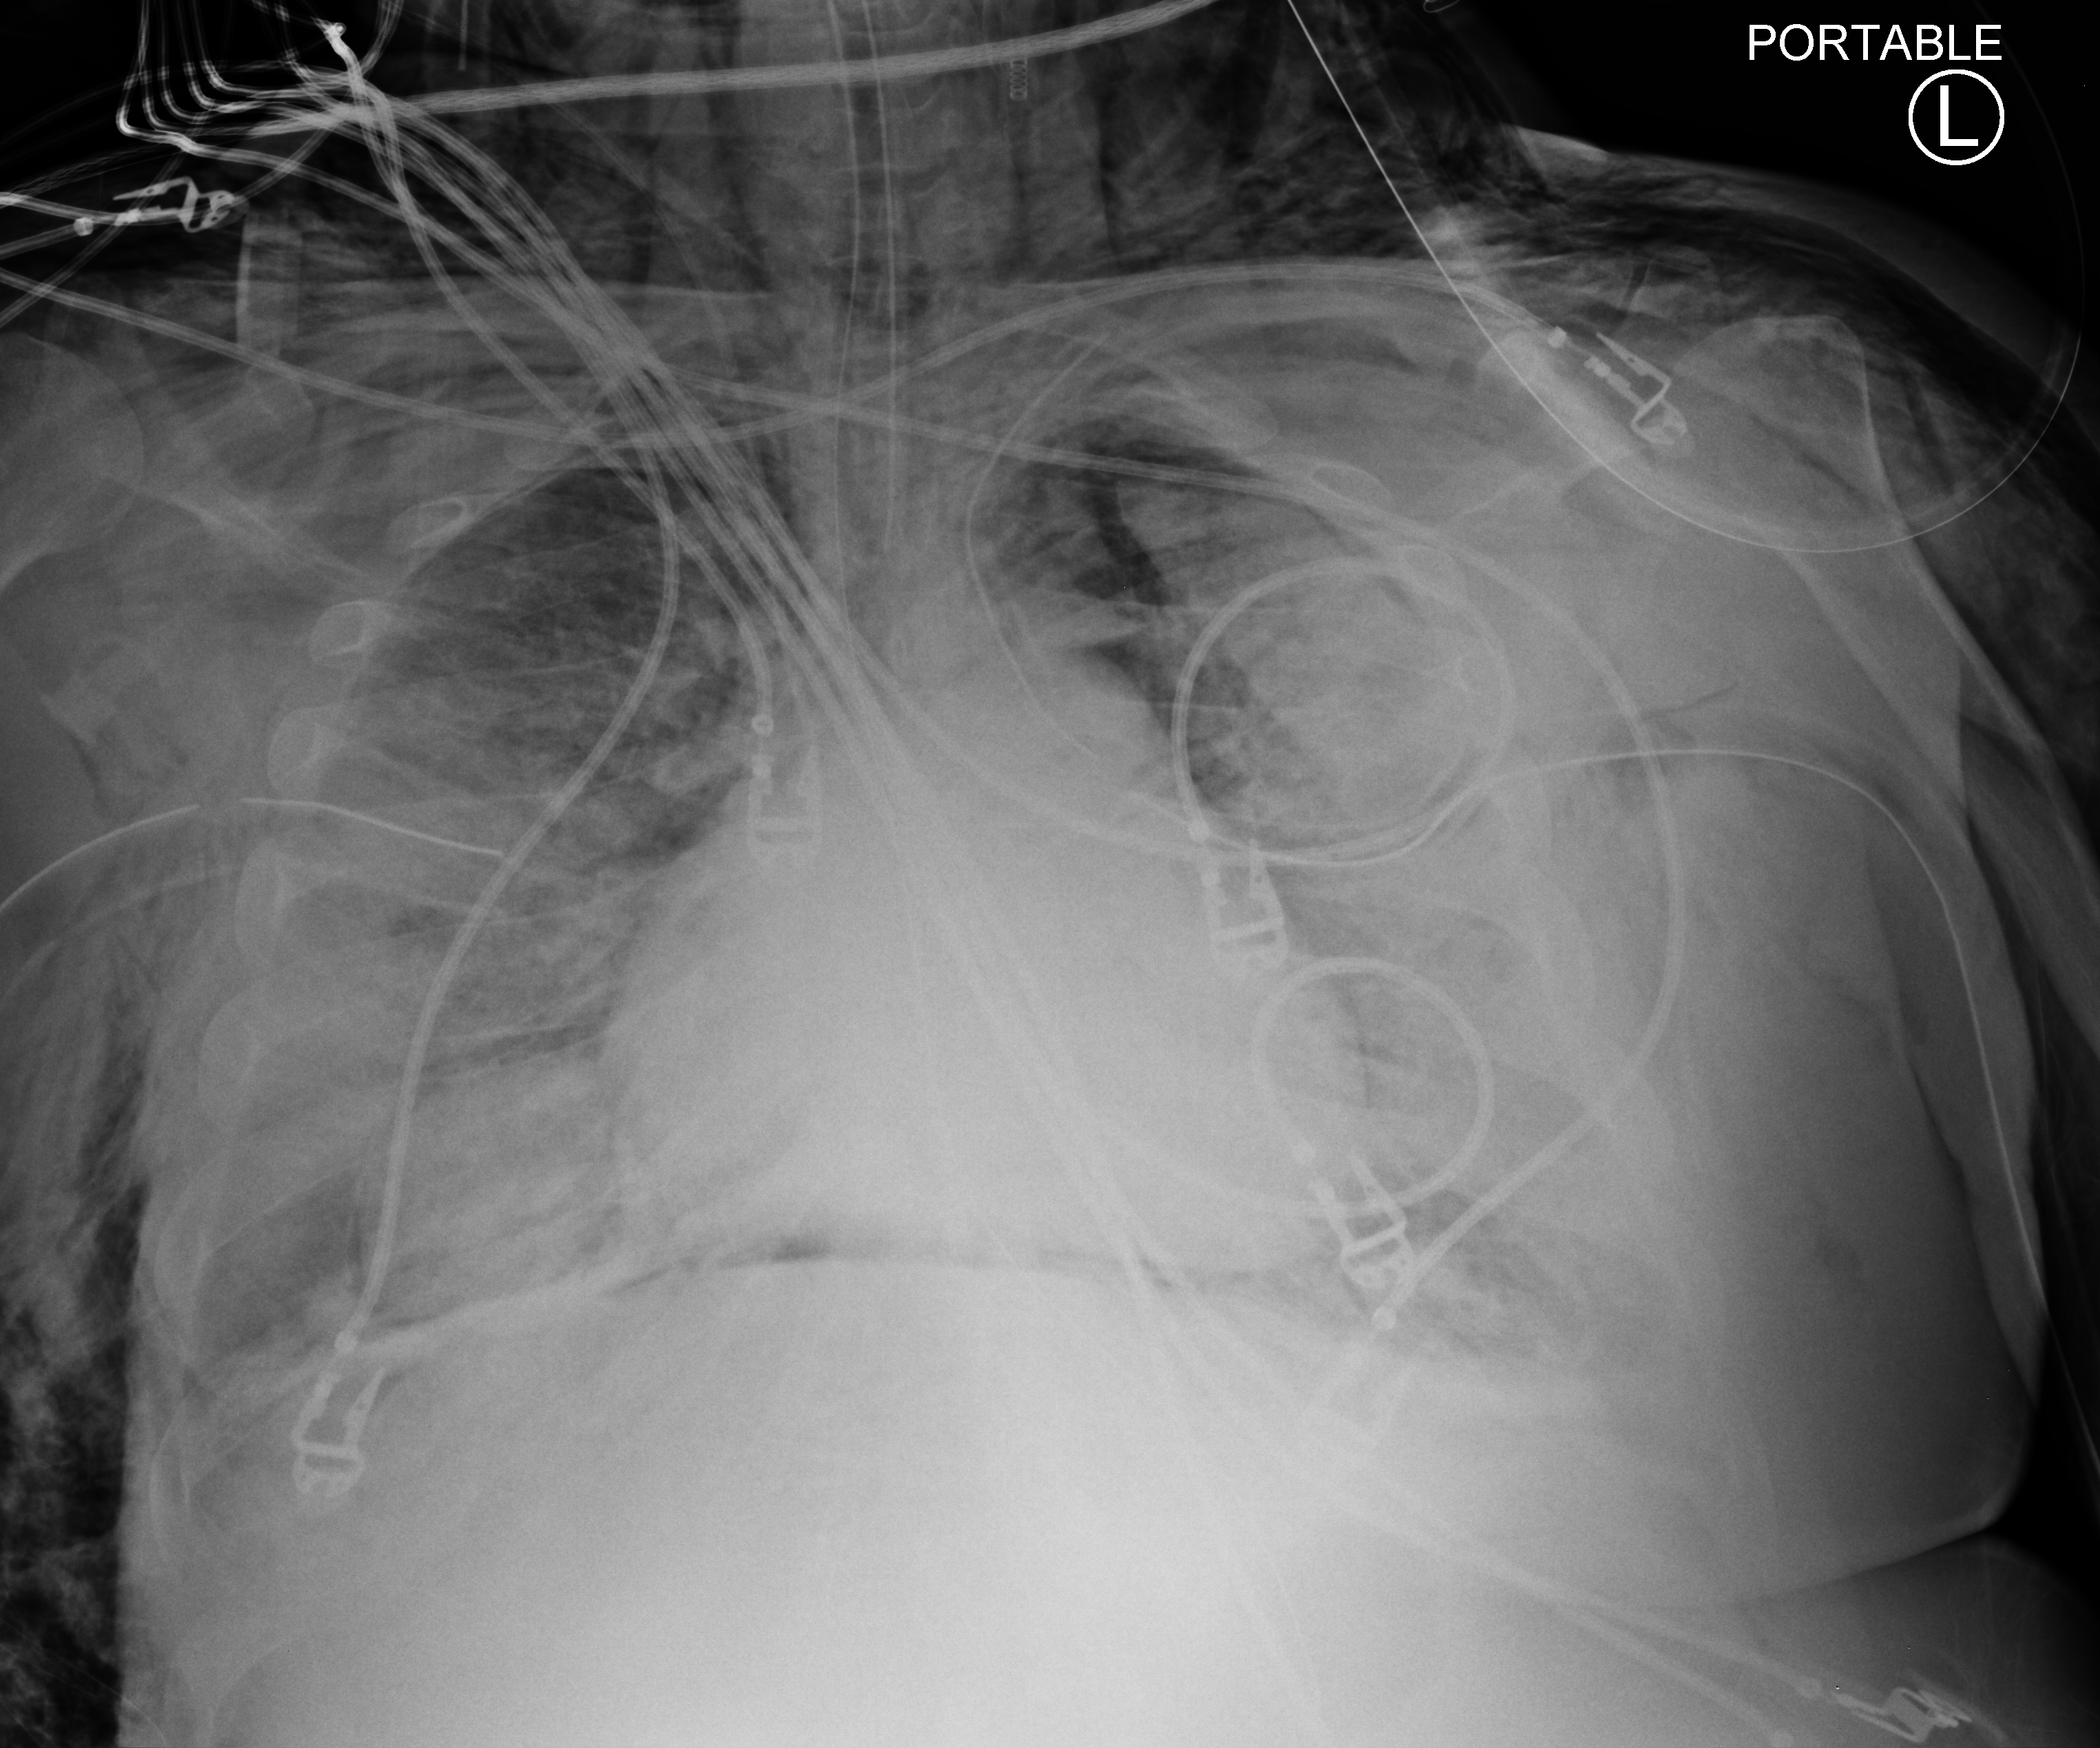
Portable chest radiograph. Adult patient hospitalised with COVID-19, age 18–59 years.
Admission-level facts for this patient (not findings on this image; timing relative to this image not recorded): admitted to intensive care during this hospital stay: yes; mechanically ventilated during this hospital stay: yes; chronic kidney disease (admission record): no.